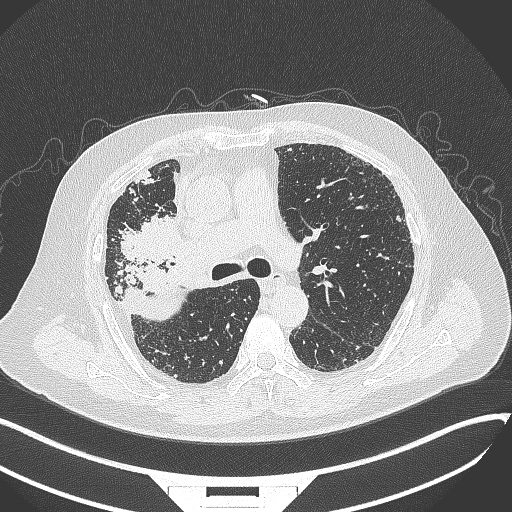
Chest CT, one axial slice; position 217 of 384 along the scan axis; lung window (W 1500 / L -600 HU); 1 mm slice thickness; 512 × 512 image matrix, field of view 400 × 400 mm. Male patient, age 69 years. From the clinical record (not read from this slice): clinical TNM (as recorded): T4 N3 M1.
Outlined on this slice (bounding box drawn by a radiologist):
- lung tumour (recorded histology: adenocarcinoma): bounding box <121,218,196,275> (left, top, right, bottom; pixels)